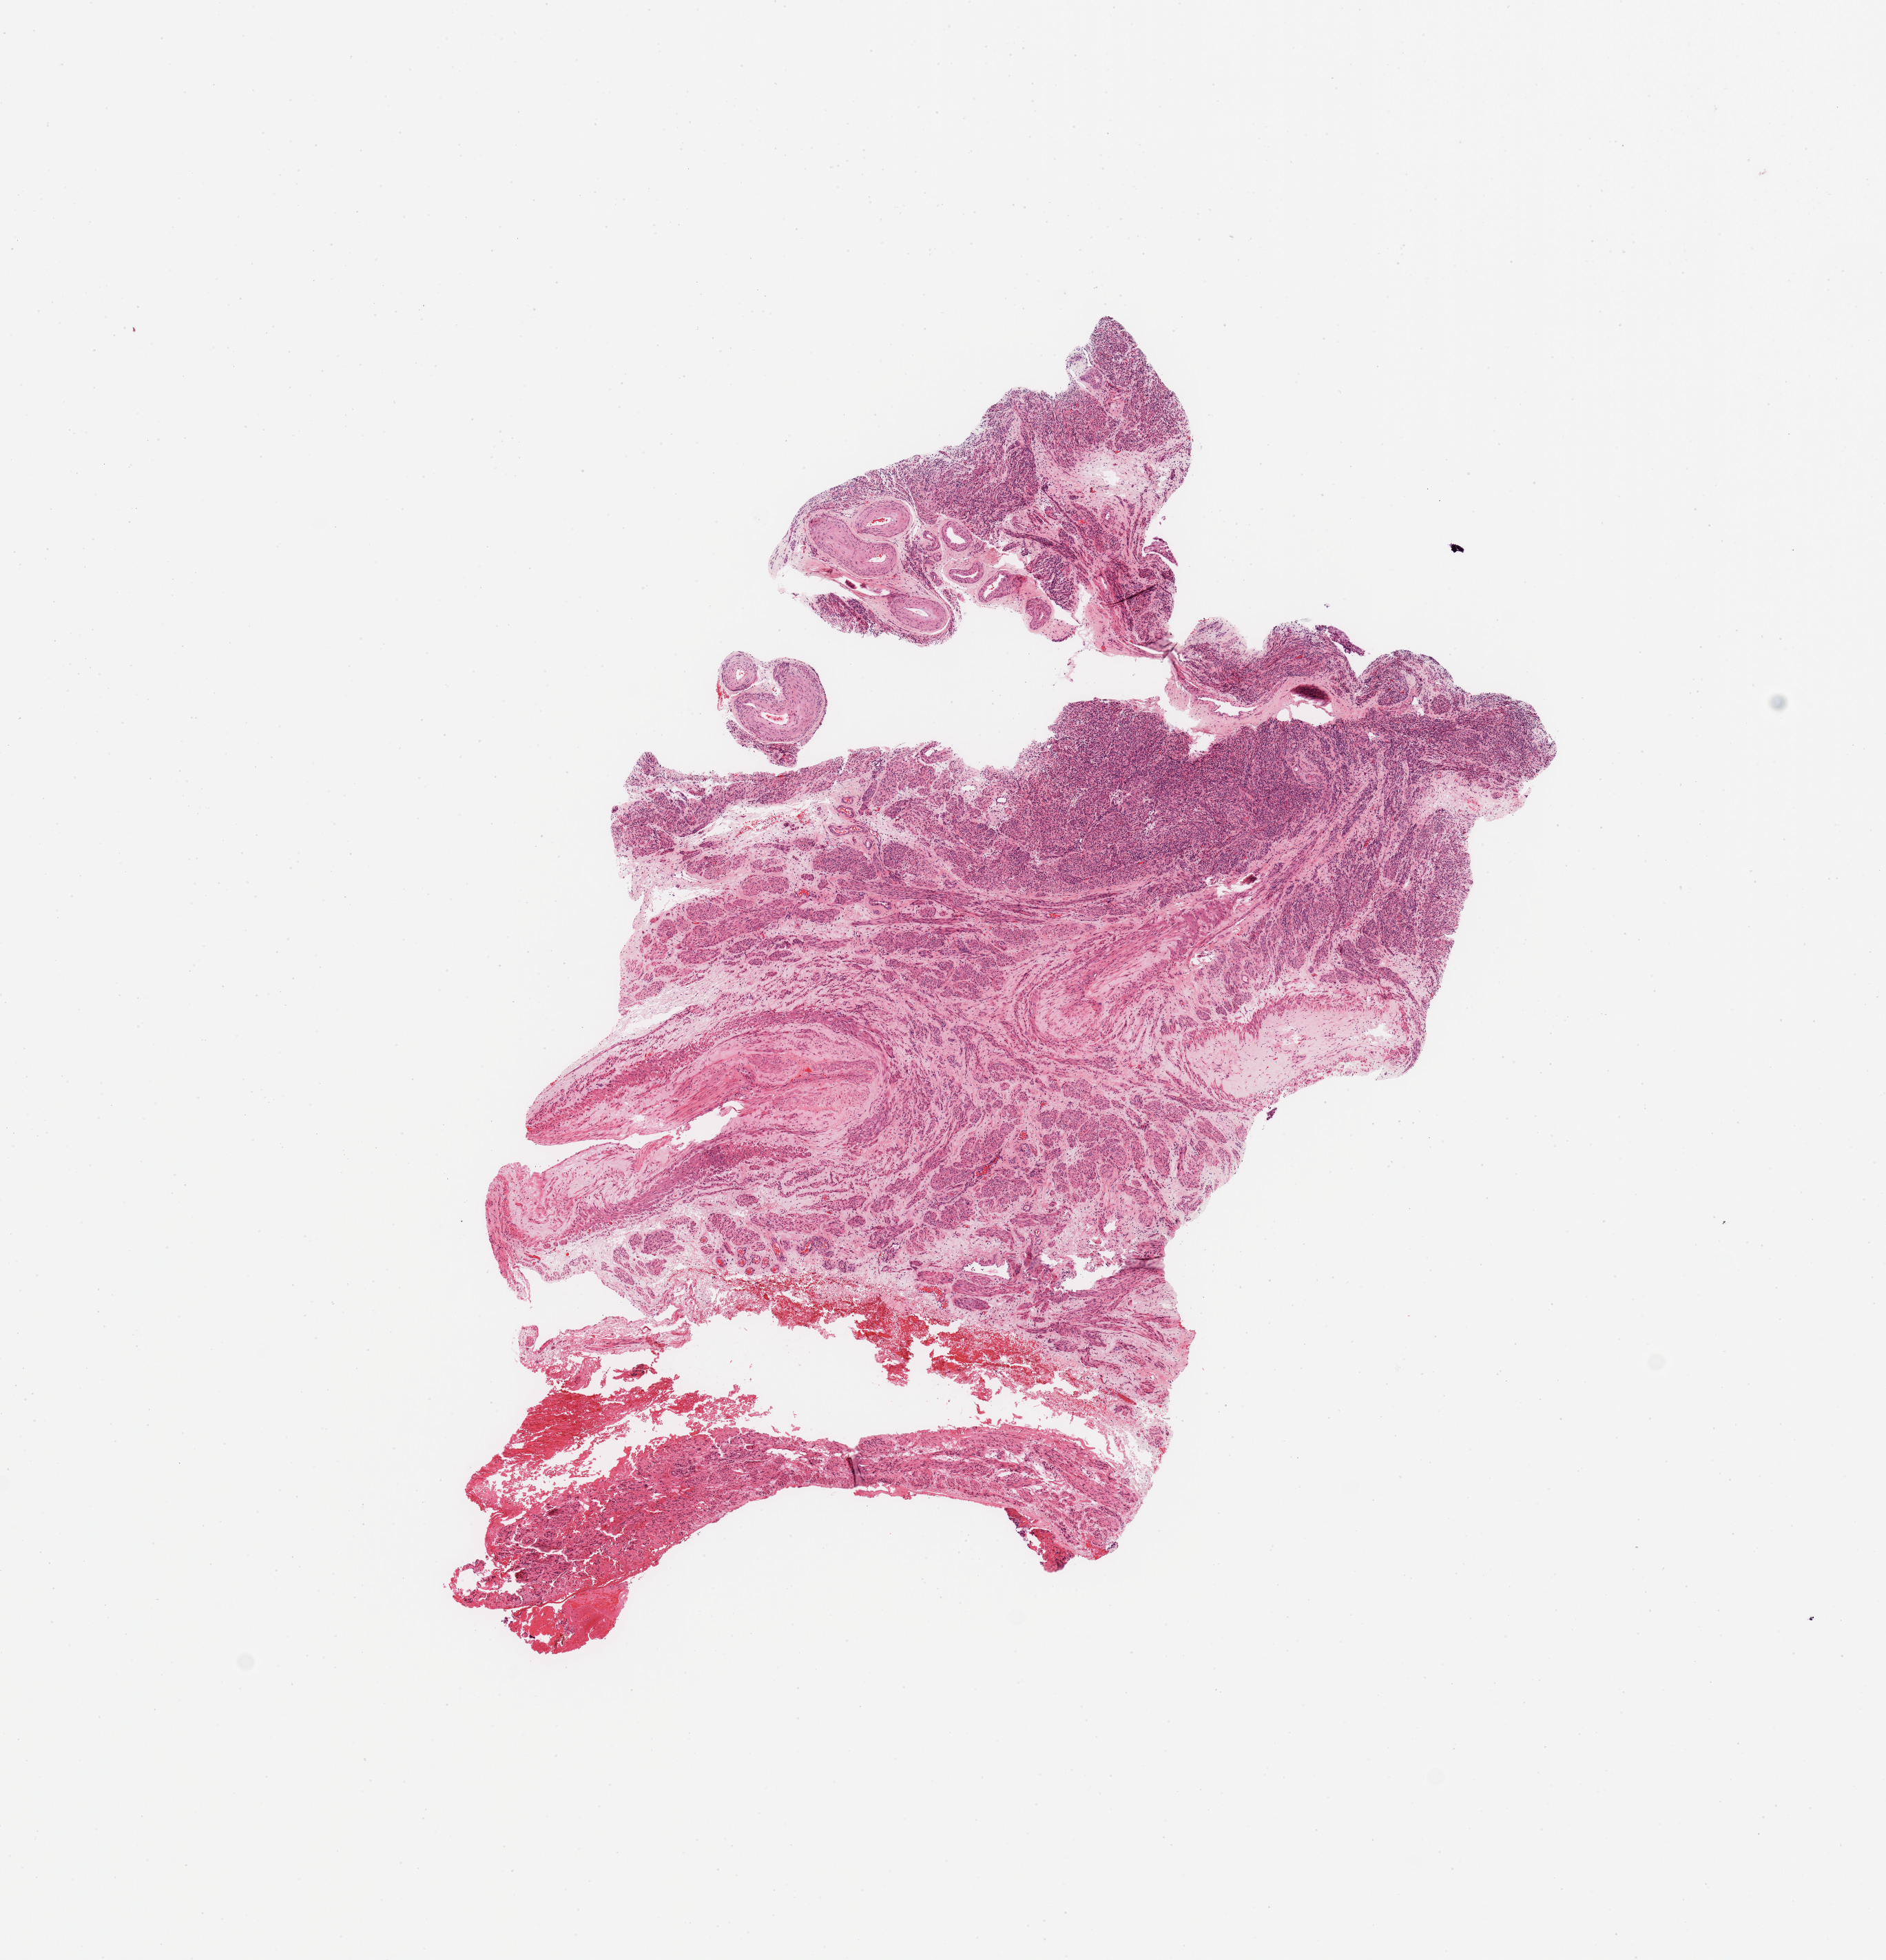
Whole-slide histology image, H&E-stained — low-resolution overview of the scanned area, about 10.8 x 11.3 mm (from a 20x scan), normal (non-tumour) tissue sample, uterus. Patient: female, age 66 years.
This section: normal (non-tumour) tissue from the same patient. Patient diagnosis: Endometrioid adenocarcinoma, NOS.